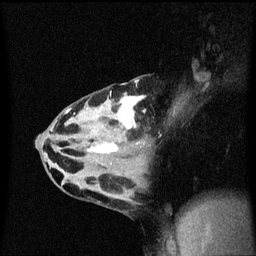
Breast MRI (dynamic contrast-enhanced), one sagittal slice. Position 30 of 60 along the scan axis. Dynamic contrast-enhanced series, image 2 of 3 at this slice position (ordered by acquisition). 1.5 T. TE 4.2 ms, TR 8.4 ms. 2 mm slice thickness. 256 × 256 image matrix. Patient: female, 32 years.
Annotated regions visible in this slice (semi-automatically segmented with operator editing):
- analysis volume of interest (the breast-tissue region the enhancement analysis was run in; not a lesion): box from (x=55, y=78) to (x=179, y=167) px
- tumour enhancement mask (voxels above the 70 % enhancement threshold inside the analysis volume of interest): (x=87, y=82)–(x=146, y=153)